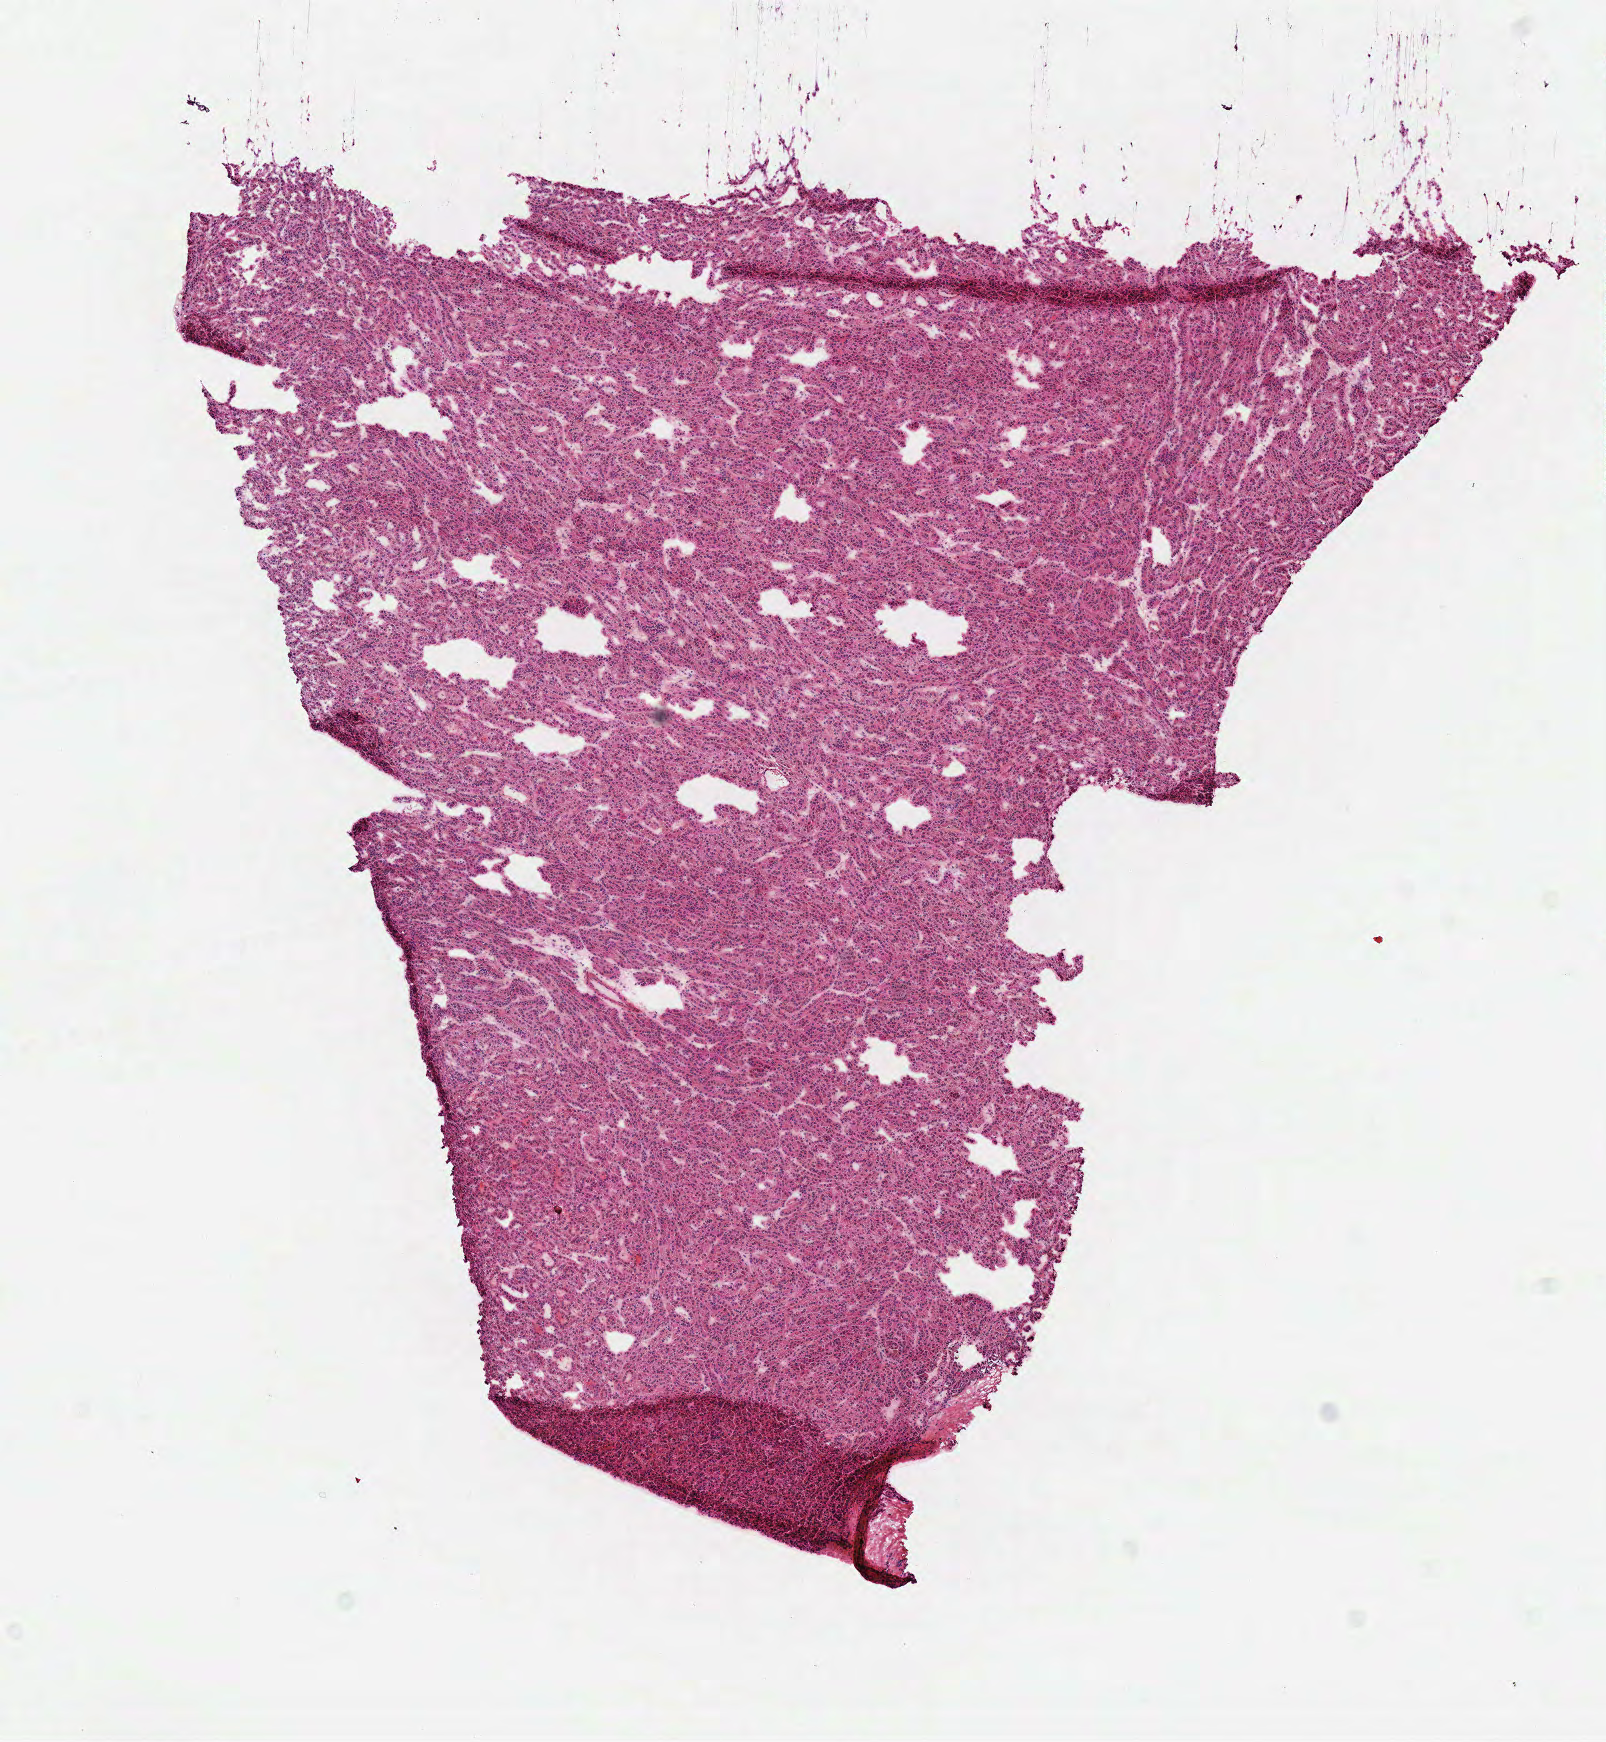
Digitized H&E tissue section (whole slide) — whole scanned area (about 6.3 x 6.9 mm) shown as a low-resolution overview, frozen section from the top of the tissue portion, kidney, primary tumour sample. Female patient; age at initial diagnosis 66 years. Slide review estimates, as recorded: tumour cells 90%, tumour nuclei 85%, normal cells 0%, stromal cells 10%, necrosis 0%.
AJCC pathologic stage: I (6th edition). Laterality: right. Diagnosis: Papillary adenocarcinoma, NOS.